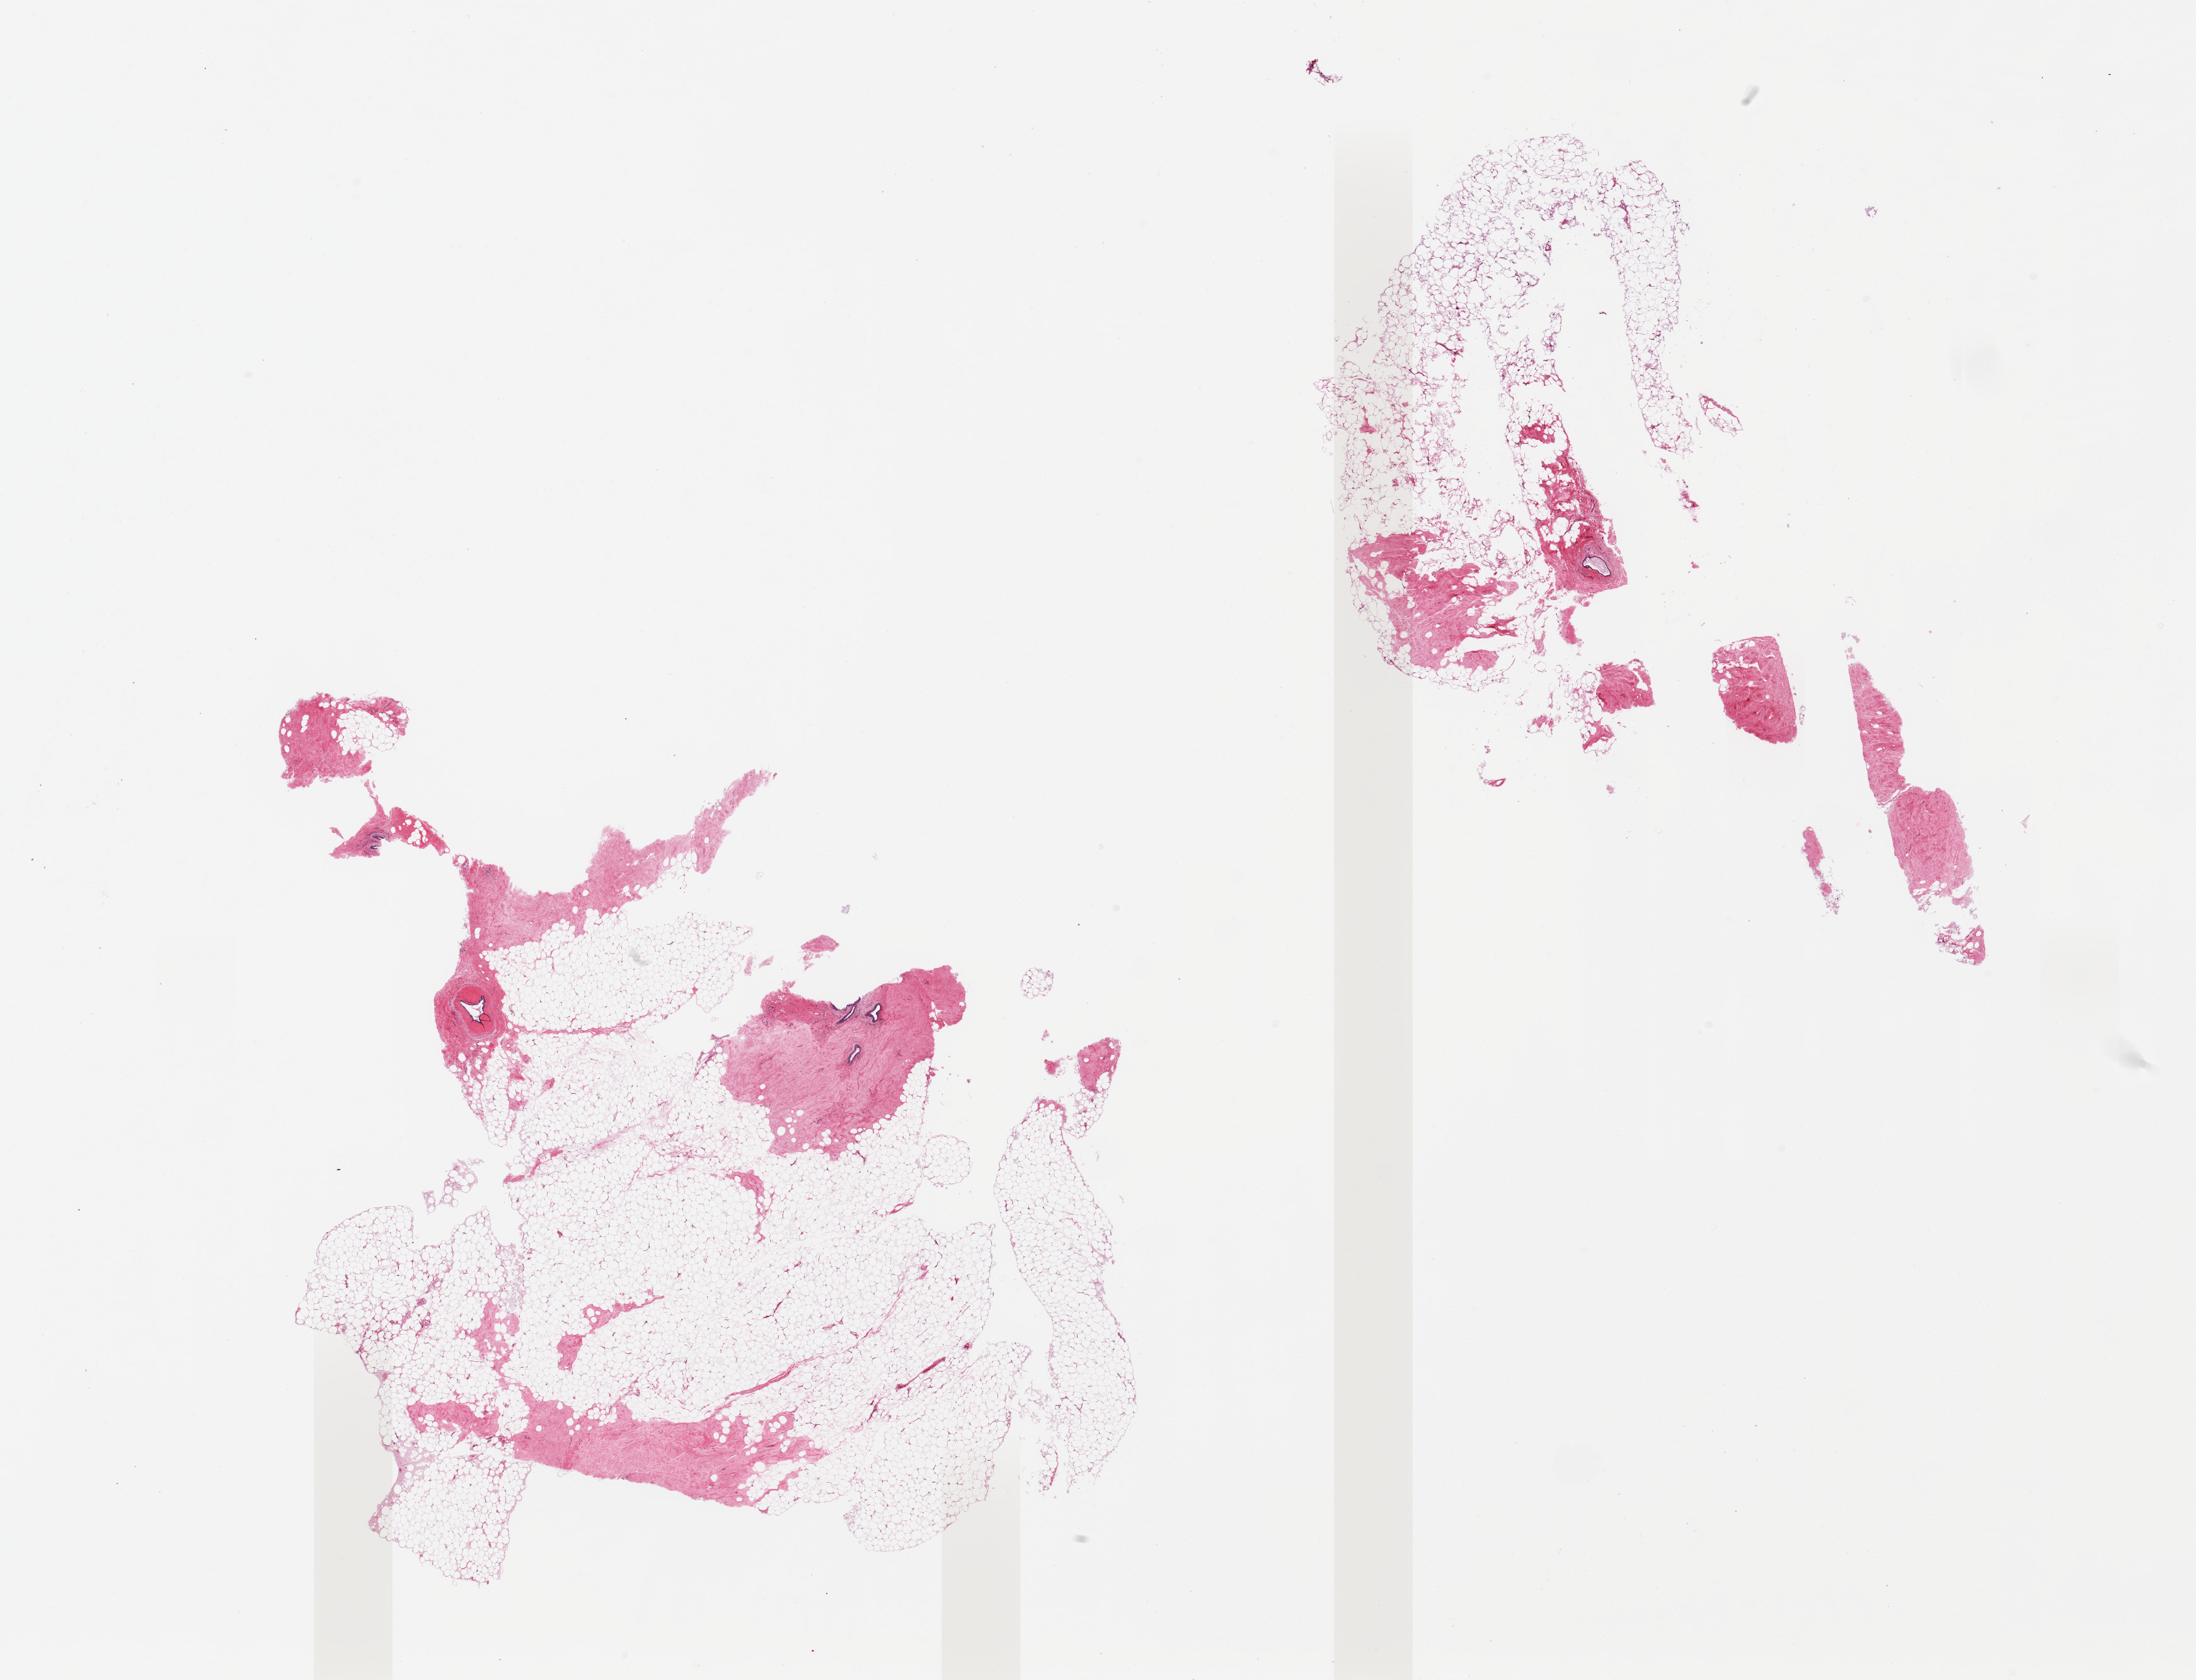
Whole-slide image, hematoxylin and eosin (H&E) stain — whole scanned area (about 27.6 x 21.1 mm) shown as a low-resolution overview; PAXgene-fixed paraffin-embedded (PFPE) section; target tissue: breast; donor tissue sample. Donor sex: female.
Reviewer comment on this tissue sample: 2 pieces, mainly fibroadipose elements, trace atrophic ductal elements; Fibrous mastopathy.